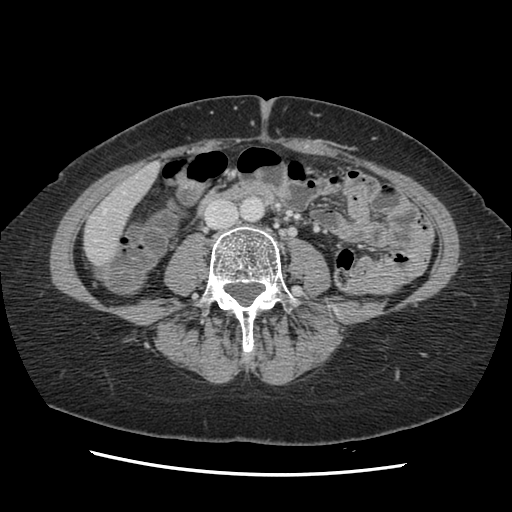
Contrast-enhanced abdominal CT, one axial slice; position 23 of 141 along the scan axis; 120 kVp; soft-tissue window (W 400 / L 40 HU); 2.5 mm slice thickness; 512 × 512 image matrix. Female patient, age 61 years. Case-level facts recorded for this patient, not image findings: diagnosis: colorectal cancer liver metastases, imaged before liver resection; multiple liver metastases: no; largest metastasis: 2.4 cm; disease in both lobes: no.
Annotated regions visible in this slice (outlined manually by an expert reader):
- hepatic veins: bounding box [x1, y1, x2, y2] px = [95, 210, 106, 241]
- liver: [85, 165, 159, 264]
- planned liver remnant (the part of the liver to remain after resection): [85, 166, 159, 264]